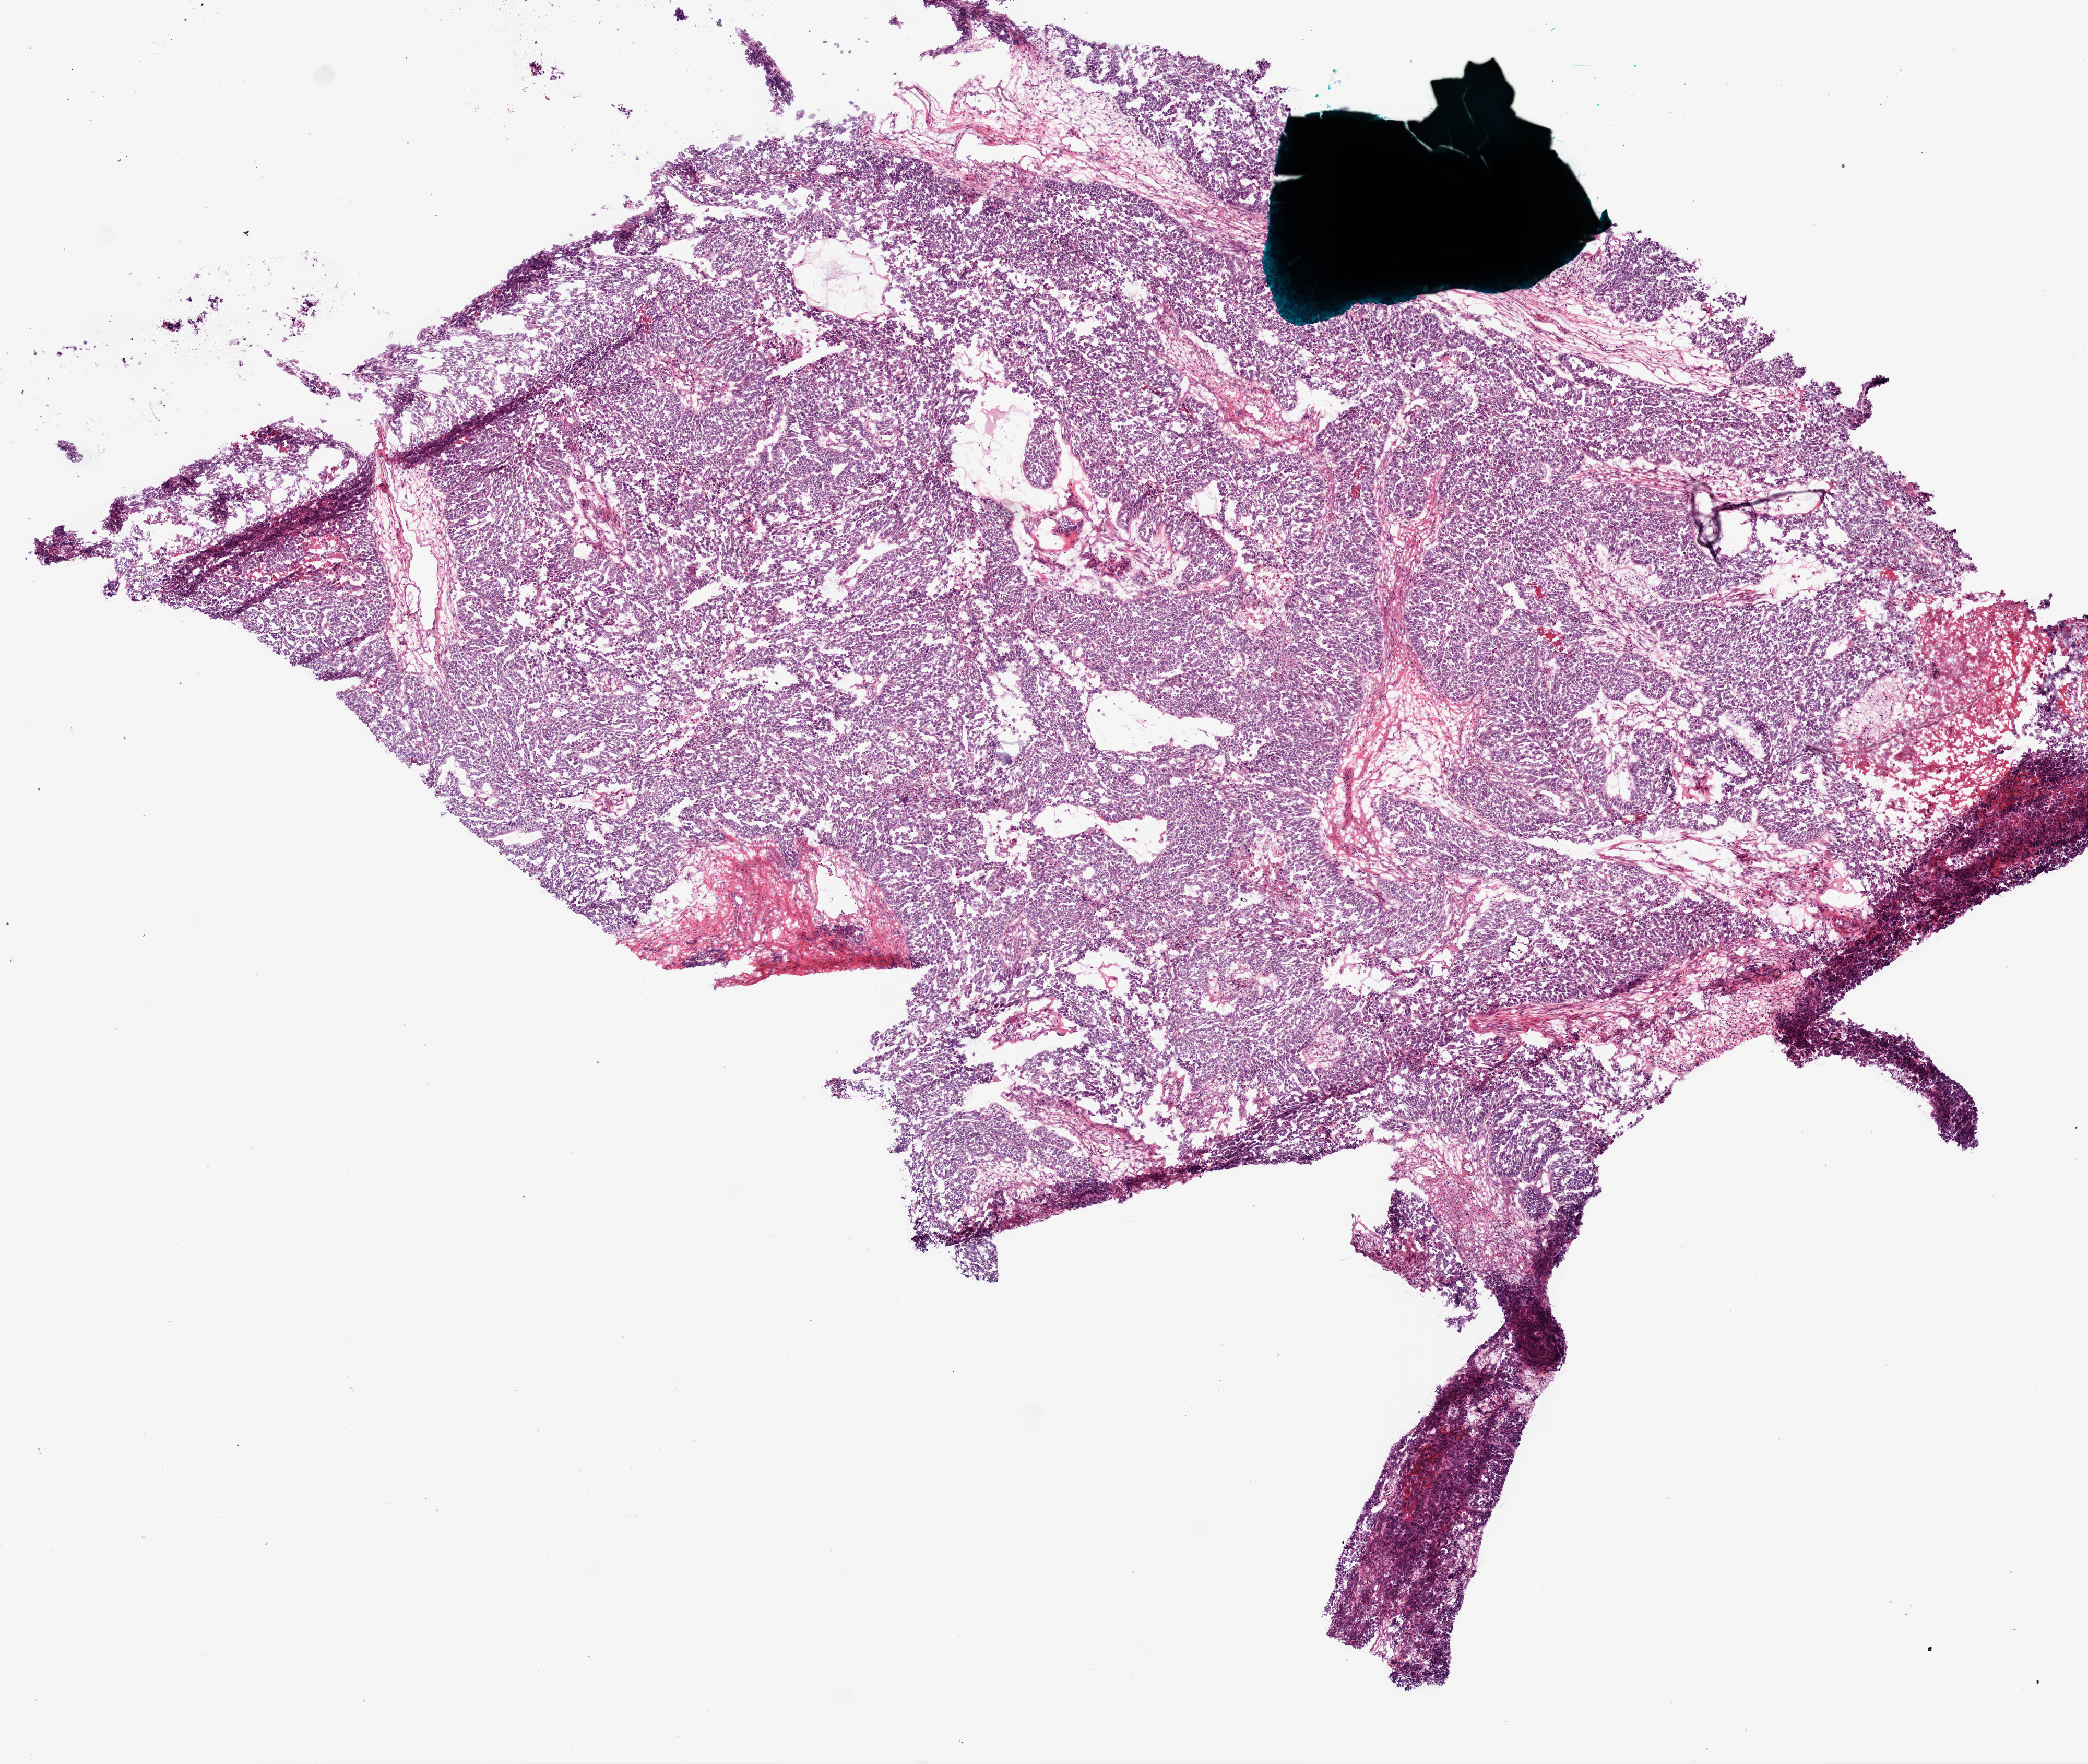
H&E whole-slide image, shown as a low-resolution overview of the whole scanned area (about 8.0 x 6.8 mm, acquisition: 20x scan); frozen section from the bottom of the tissue portion; ovary, primary tumour sample. Patient: female, age at initial diagnosis 67 years.
Pathologic diagnosis: Serous cystadenocarcinoma, NOS.